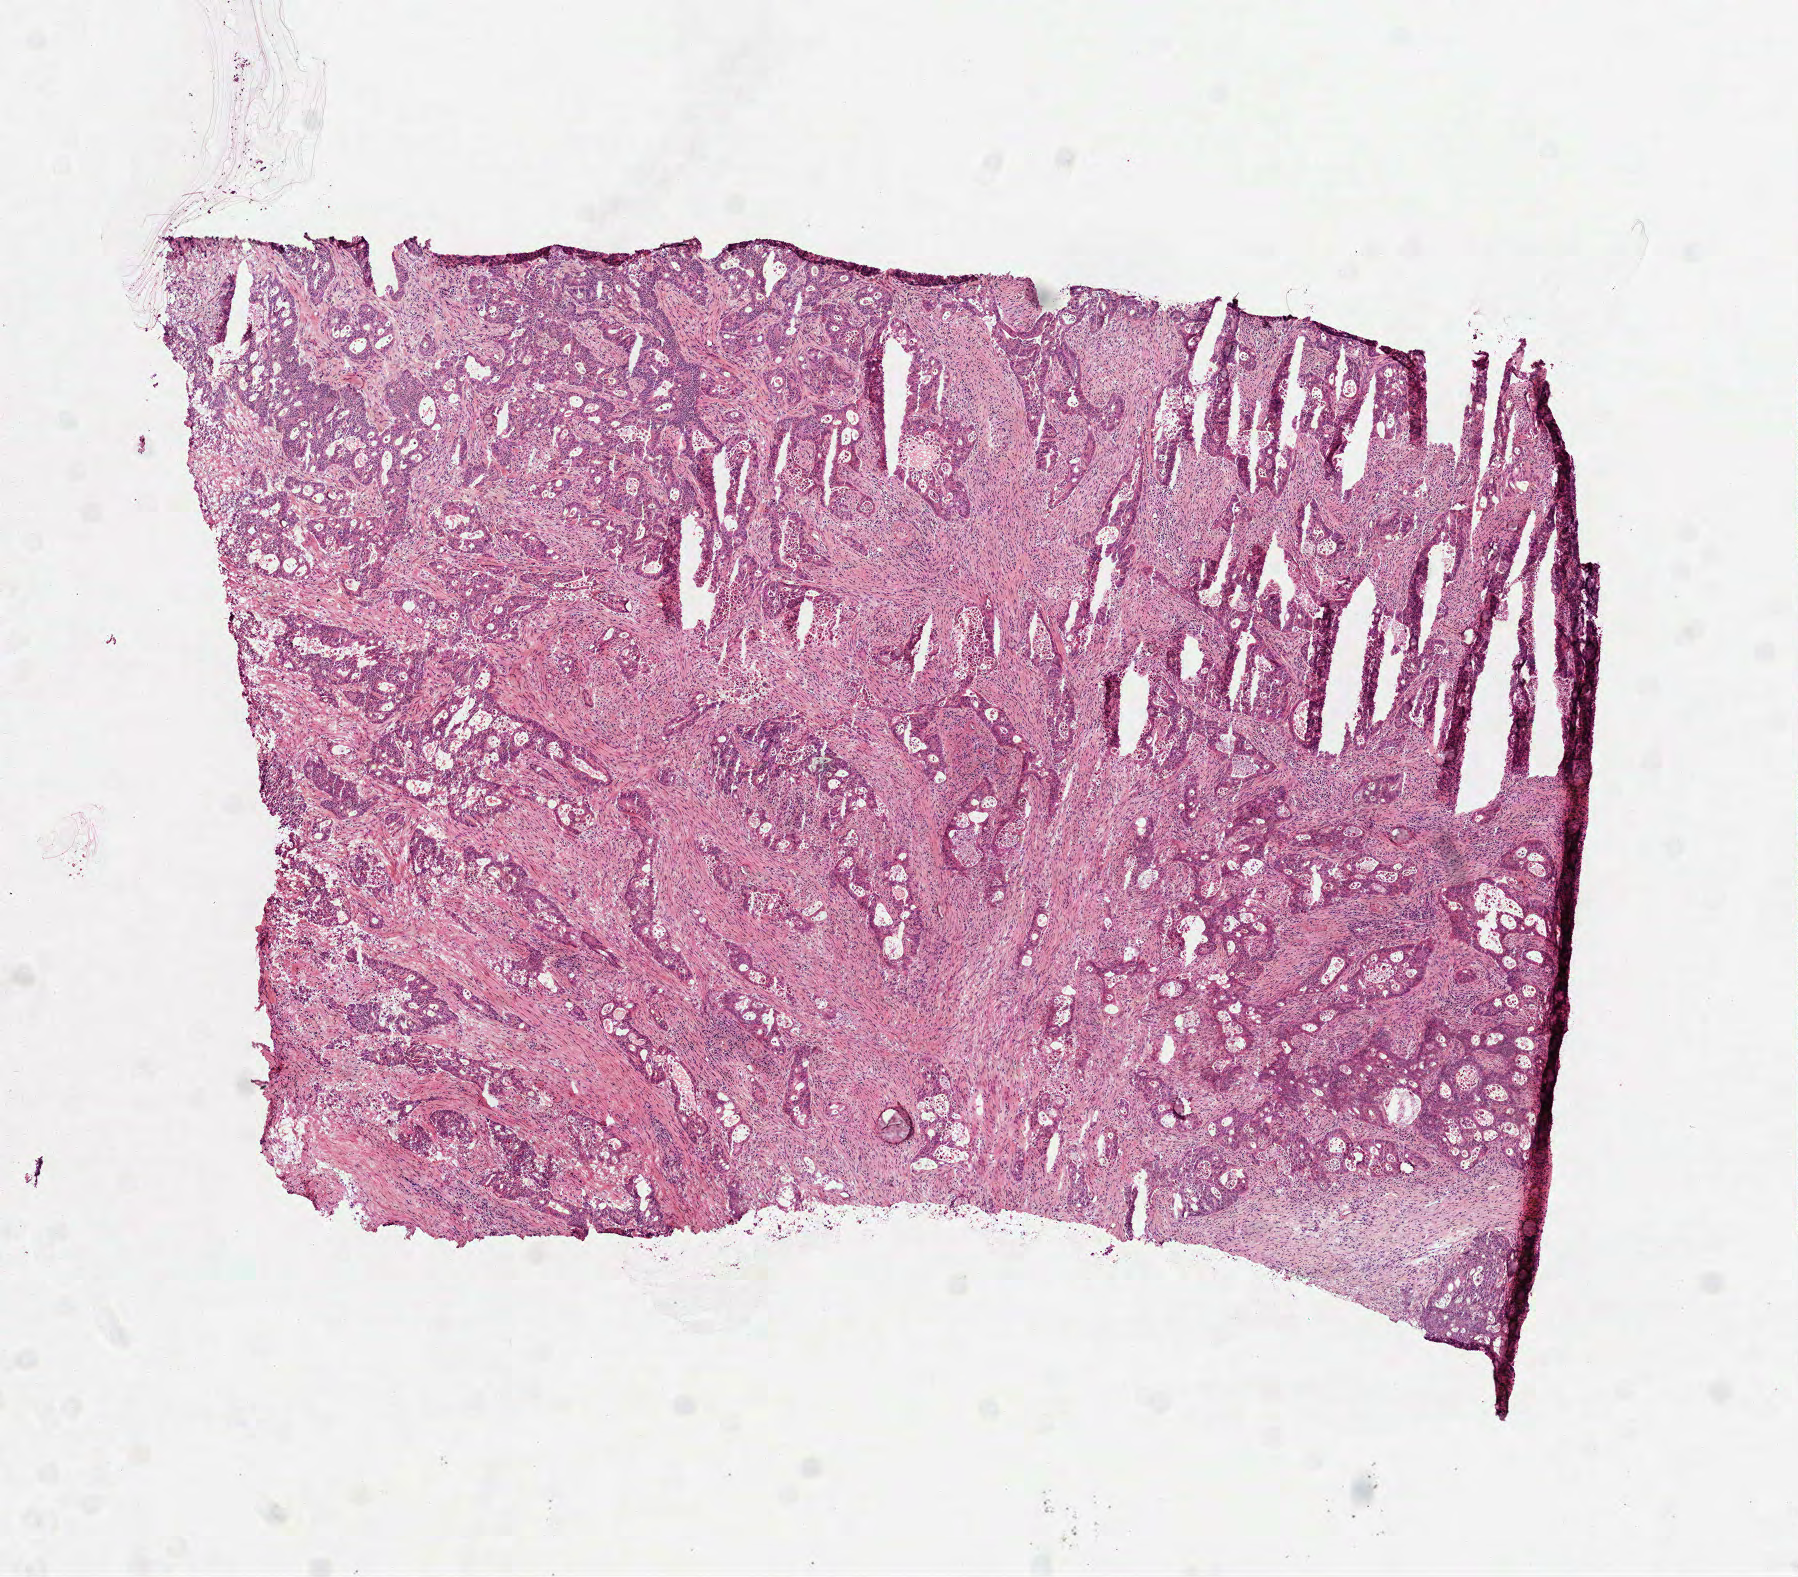
Whole-slide histology image, Hematoxylin and eosin (H&E) stained — shown as a low-resolution overview of the whole scanned area (about 7.3 x 6.4 mm, slide scanned at 40x), frozen section, sample: primary tumour, colon. Male patient; age at initial diagnosis 49 years. Slide review estimates, as recorded: tumour cells 99%, tumour nuclei 65%, normal cells 0%, stromal cells 0%, necrosis 1%. Infiltration values recorded for this section: lymphocyte infiltration 15%, monocyte infiltration 1%, neutrophil infiltration 5%.
Pathologic diagnosis: Adenocarcinoma, NOS (splenic flexure of colon). AJCC pathologic stage: IIA. Lymph nodes positive (case pathology): 0 of 13 examined.